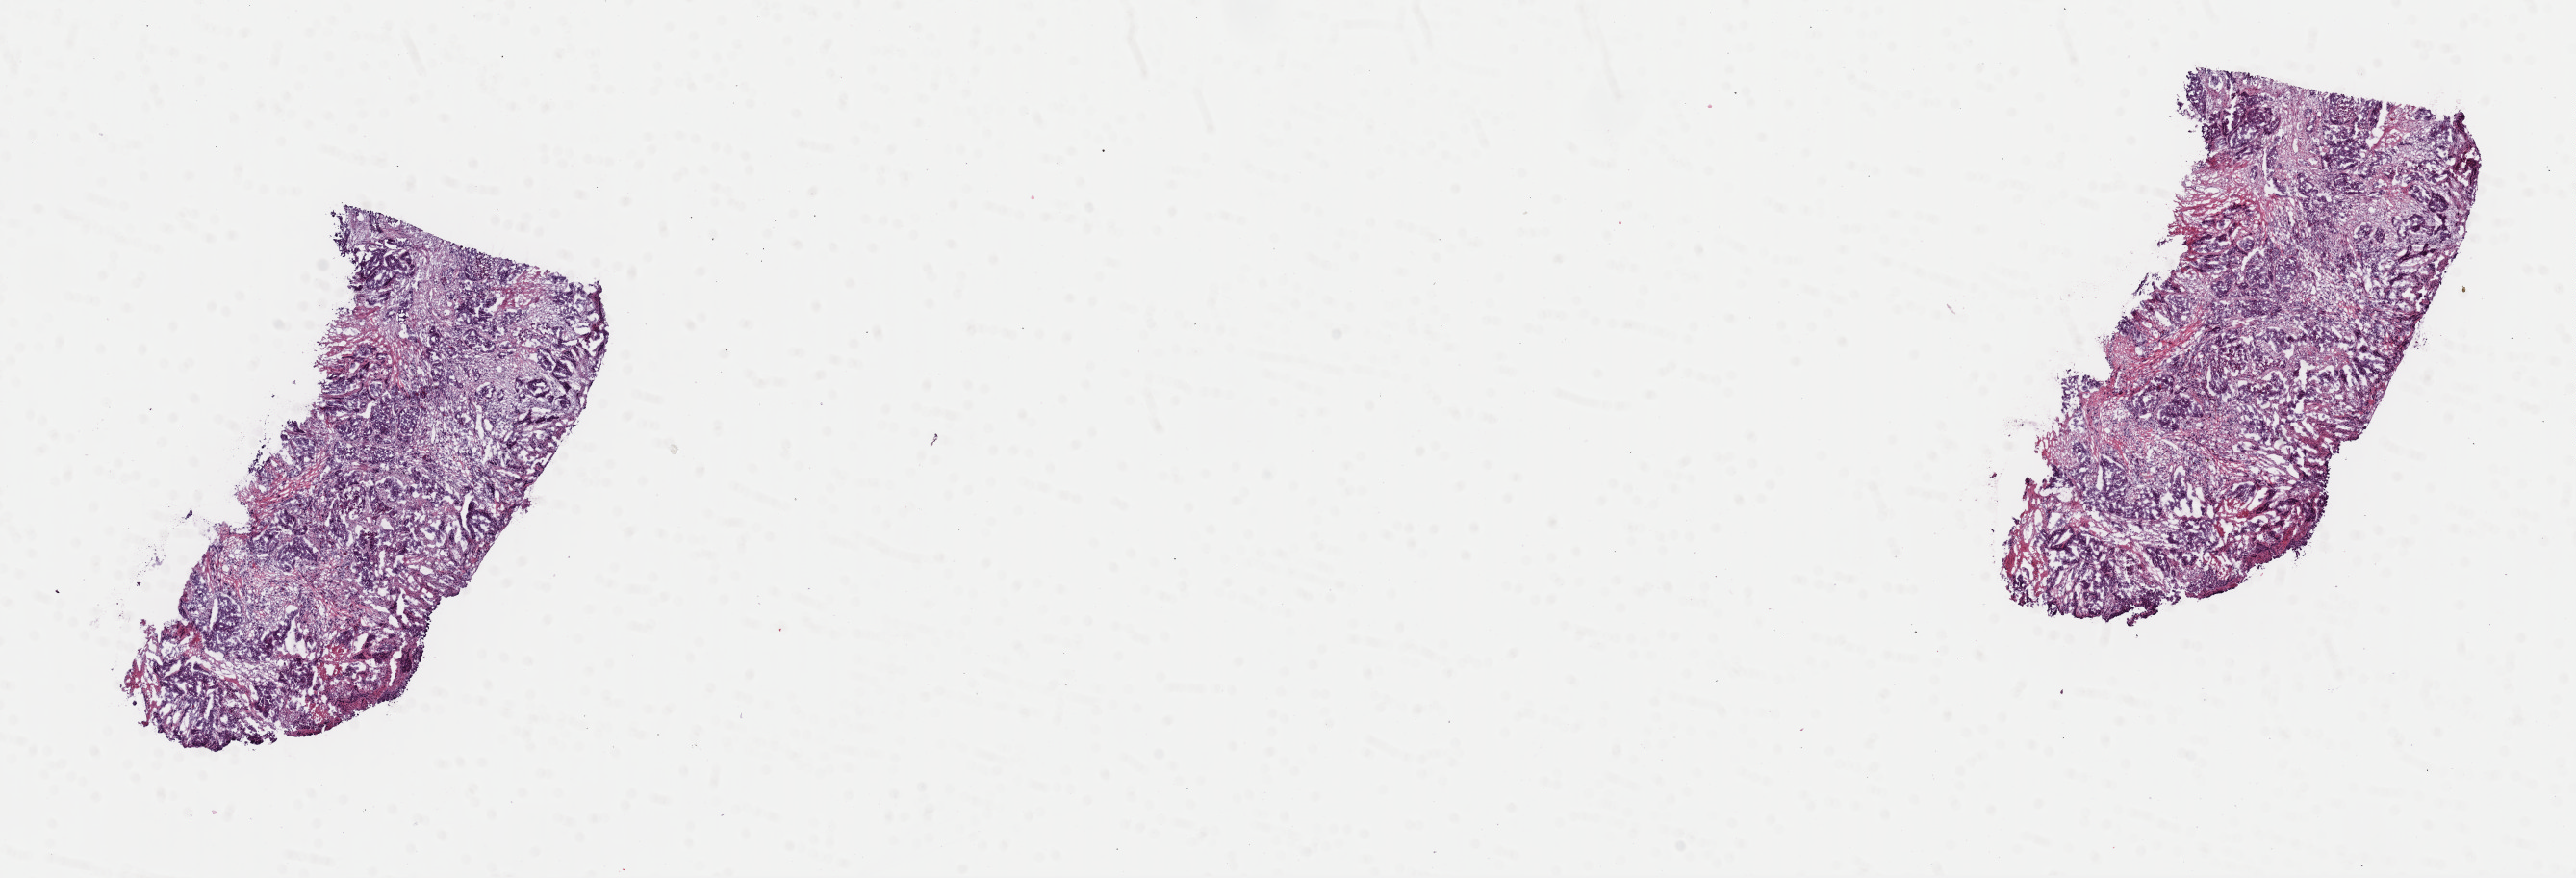
Digitized H&E tissue section (whole slide) — shown as a low-resolution overview of the whole scanned area (about 21.1 x 7.2 mm, acquisition: 40x scan). Frozen section. Ovary, primary tumour sample. Patient: female, age at initial diagnosis 55 years. Histologic grade: G3 (poorly differentiated). Composition of this section per pathologist review: tumour cells 60%, tumour nuclei 60%, normal cells 0%, stromal cells 30%, necrosis 10%. Infiltration values recorded for this section: lymphocyte infiltration 40%, monocyte infiltration 20%, neutrophil infiltration 20%.
Pathologic diagnosis: Serous cystadenocarcinoma, NOS. Laterality: right. FIGO stage: IC.